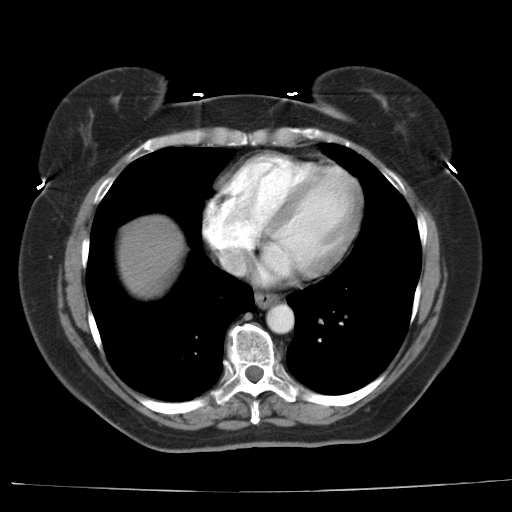
Contrast-enhanced abdominal CT, one axial slice; reconstruction kernel AA-1; 140 kVp; soft-tissue window (W 400 / L 40 HU); 5 mm slice thickness; 512 × 512 image matrix. Female patient. From the clinical record (not read from this slice): diagnosis: colorectal cancer liver metastases, imaged before liver resection; multiple liver metastases: yes; largest metastasis: 1.8 cm; disease in both lobes: no.
Annotated regions visible in this slice (manually delineated by an expert):
- liver: bounding box <117,215,186,297> (left, top, right, bottom; pixels)